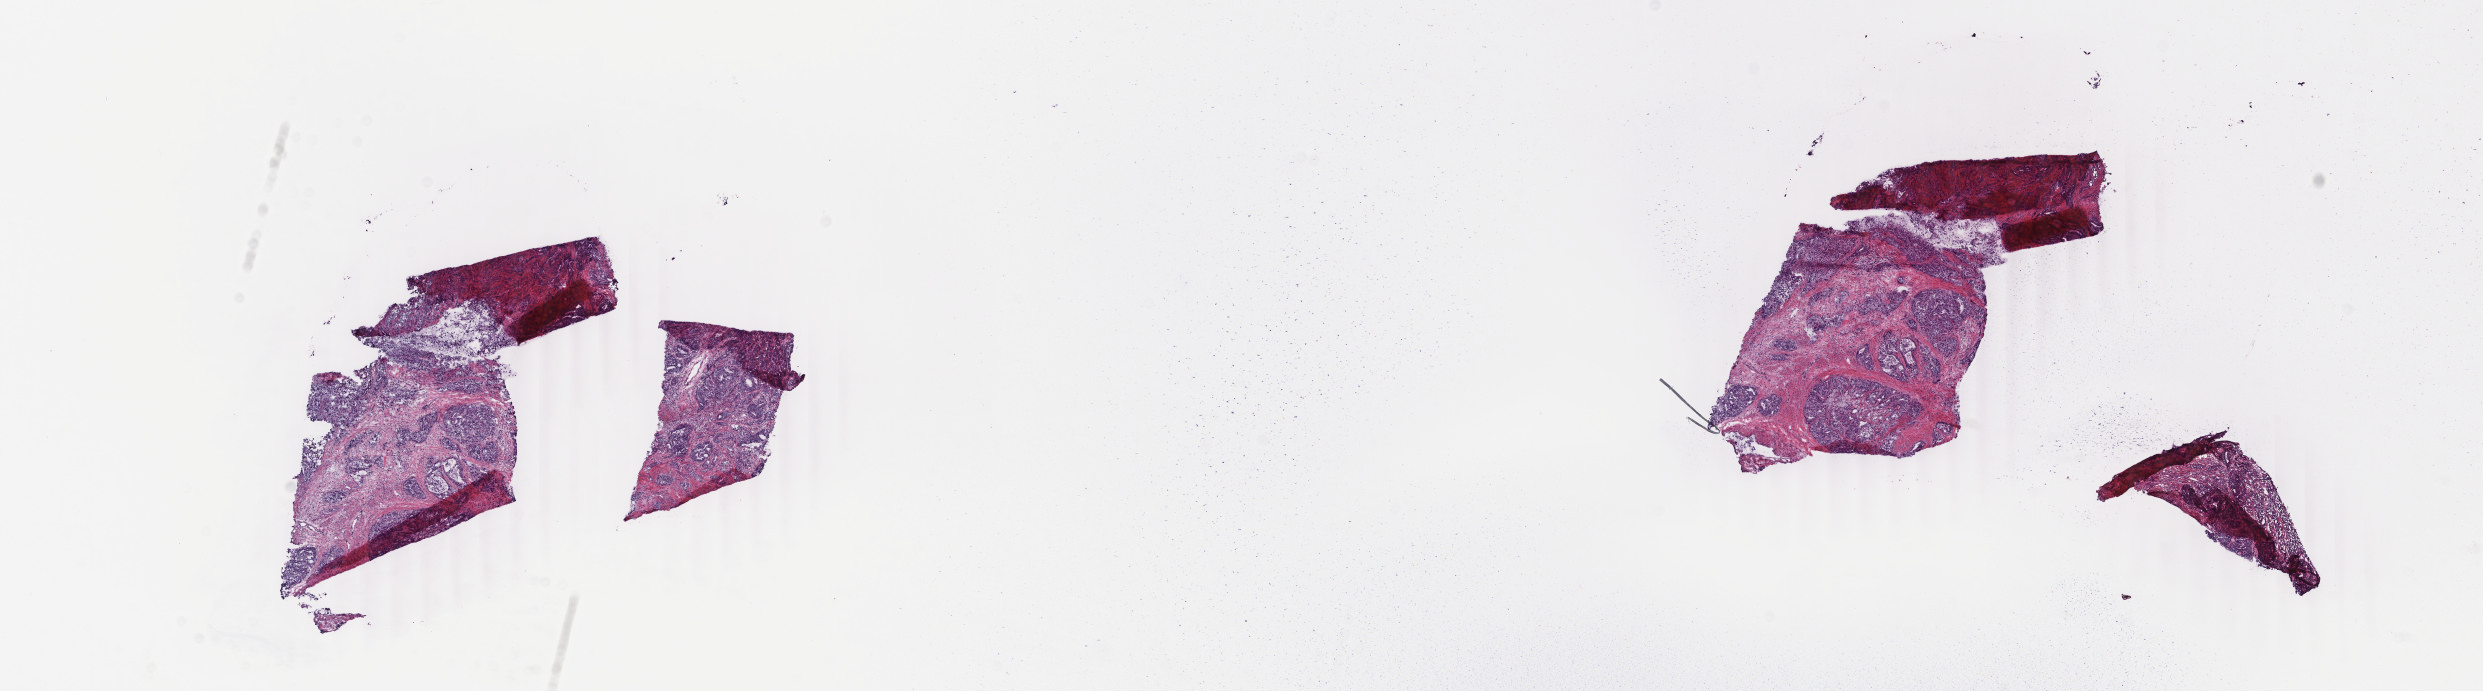
Digitized H&E tissue section (whole slide) — shown as a low-resolution overview of the whole scanned area (about 19.8 x 5.5 mm); frozen section from the top of the tissue portion; sample: primary tumour, uterus. Patient: female, age at initial diagnosis 63 years.
Diagnosis: Endometrioid adenocarcinoma, NOS.